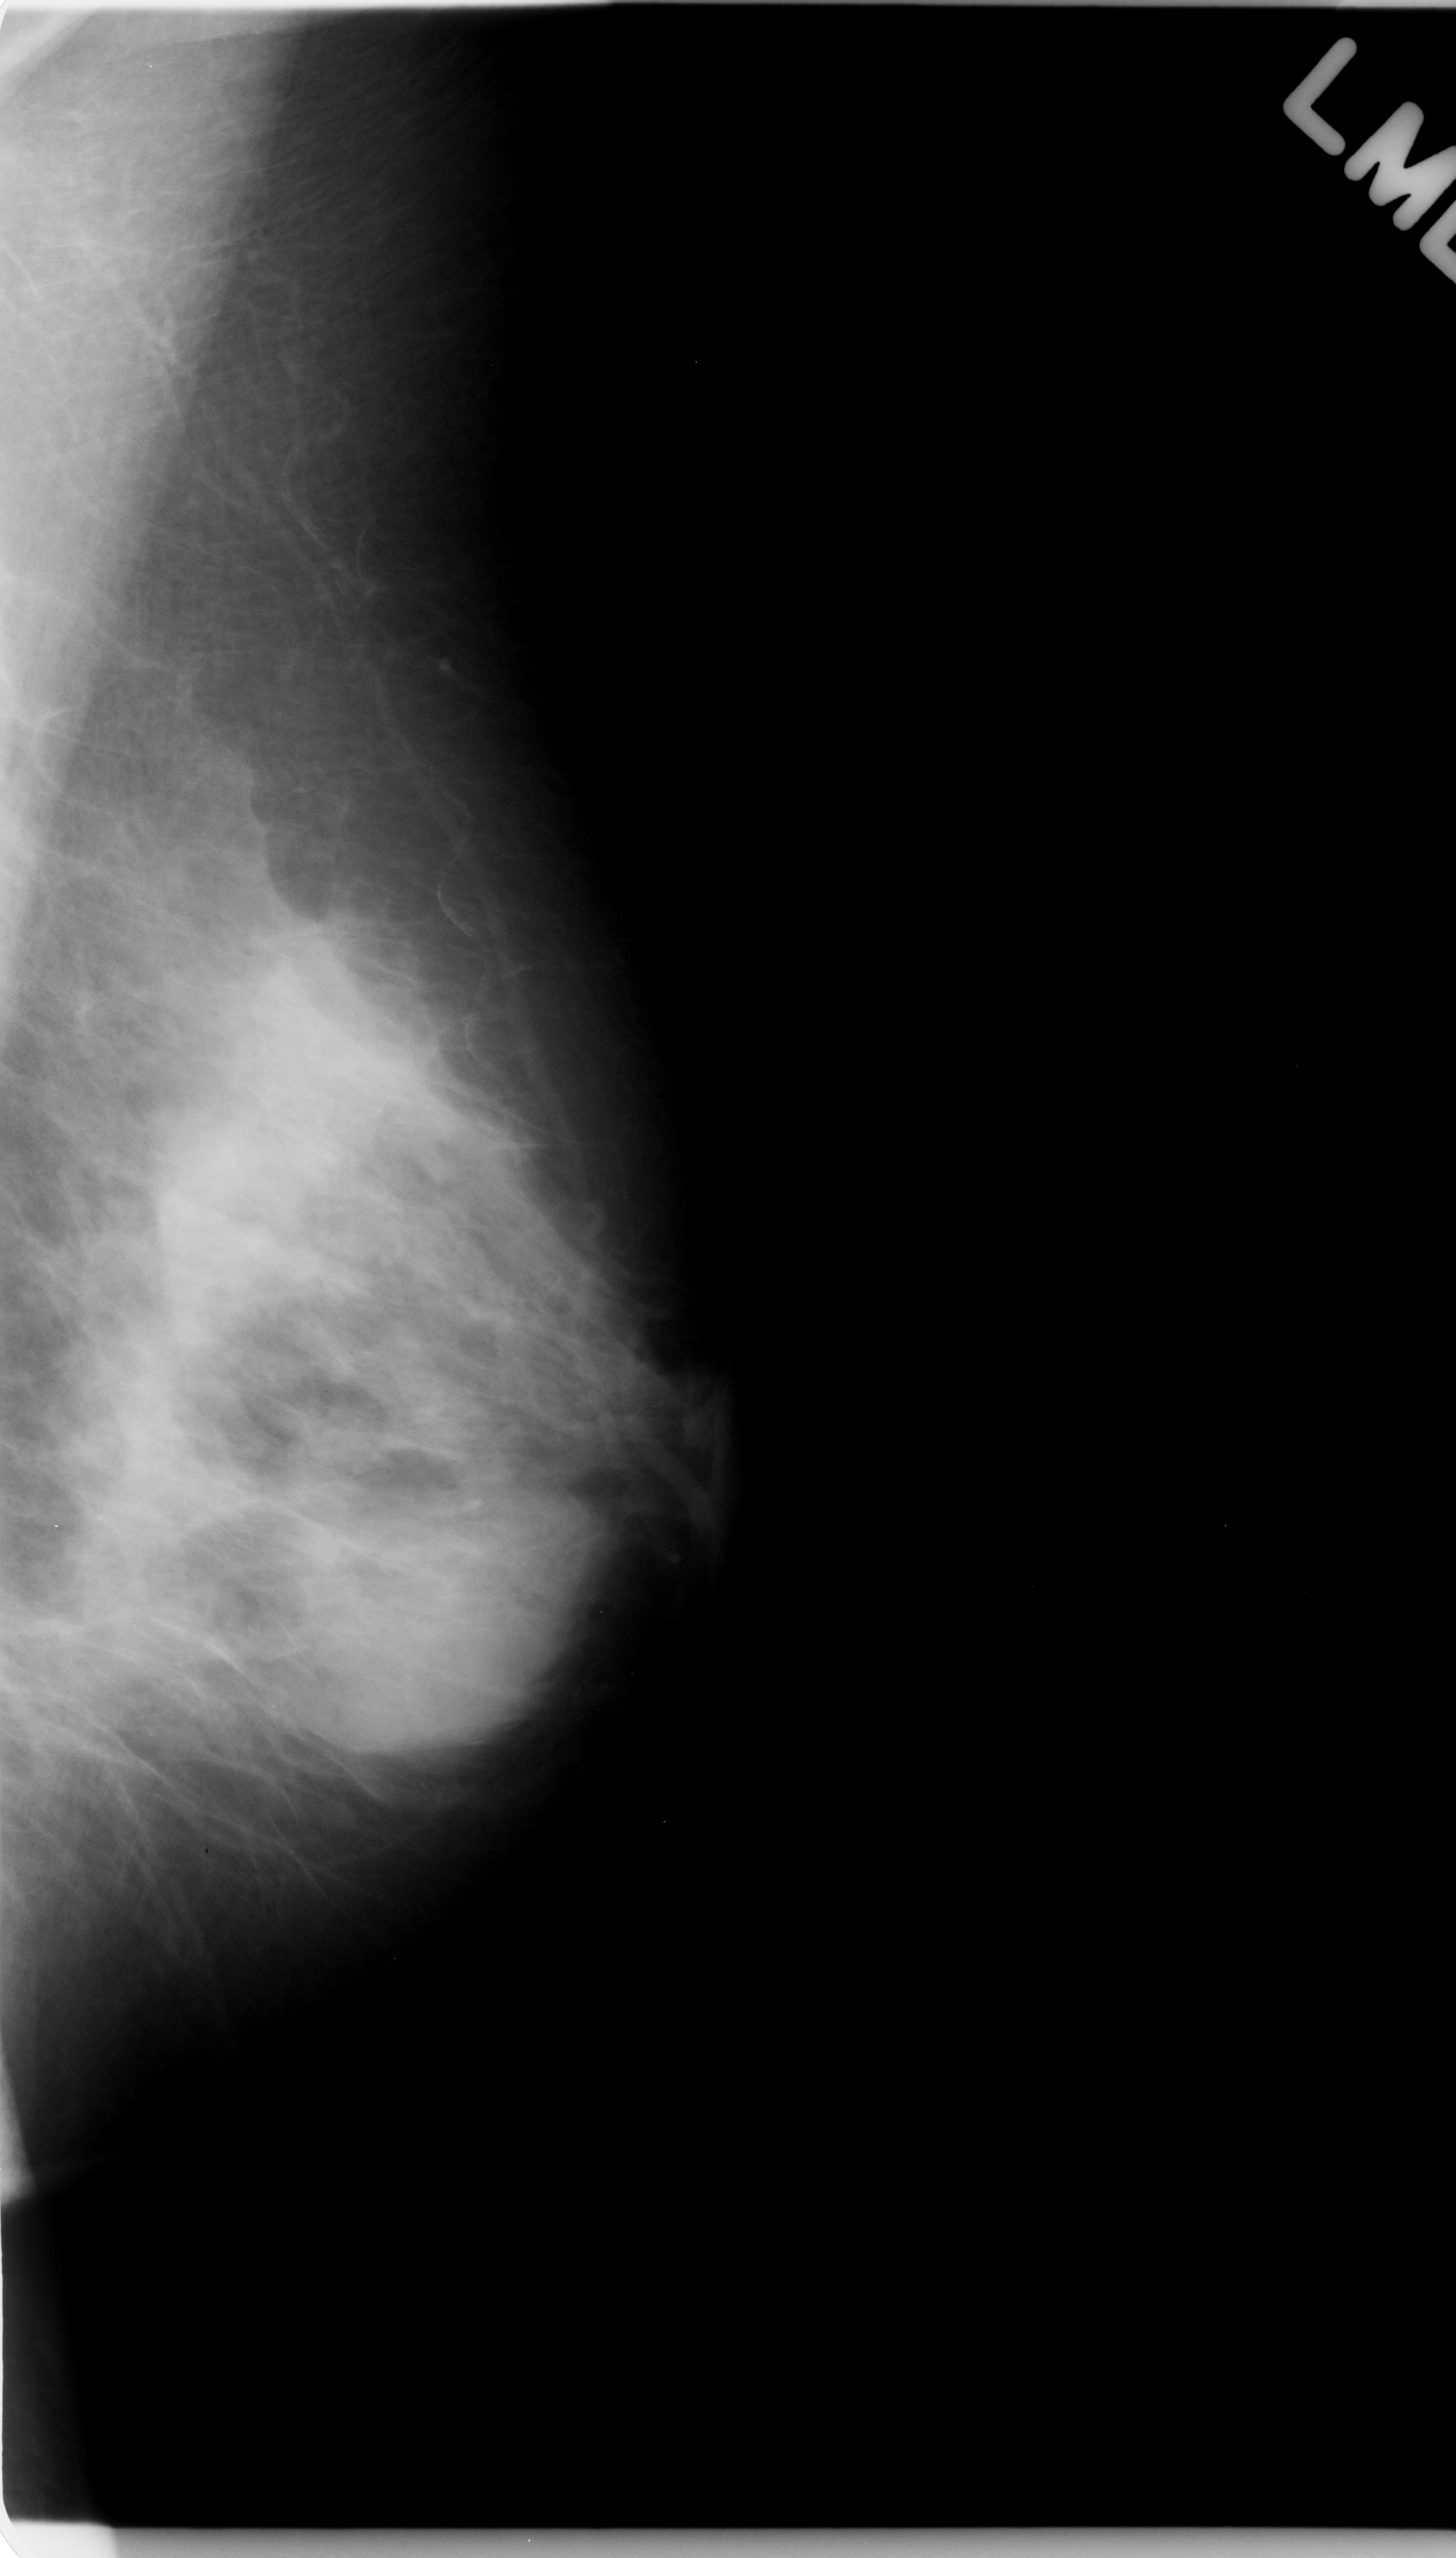
Digitized screen-film mammogram; left breast; mediolateral oblique (MLO) view.
Finding: mass, shape oval, margins ill defined; BI-RADS assessment category 3; subtlety rating 4 on a 1 (subtle) to 5 (obvious) scale; pathology (as recorded): benign.